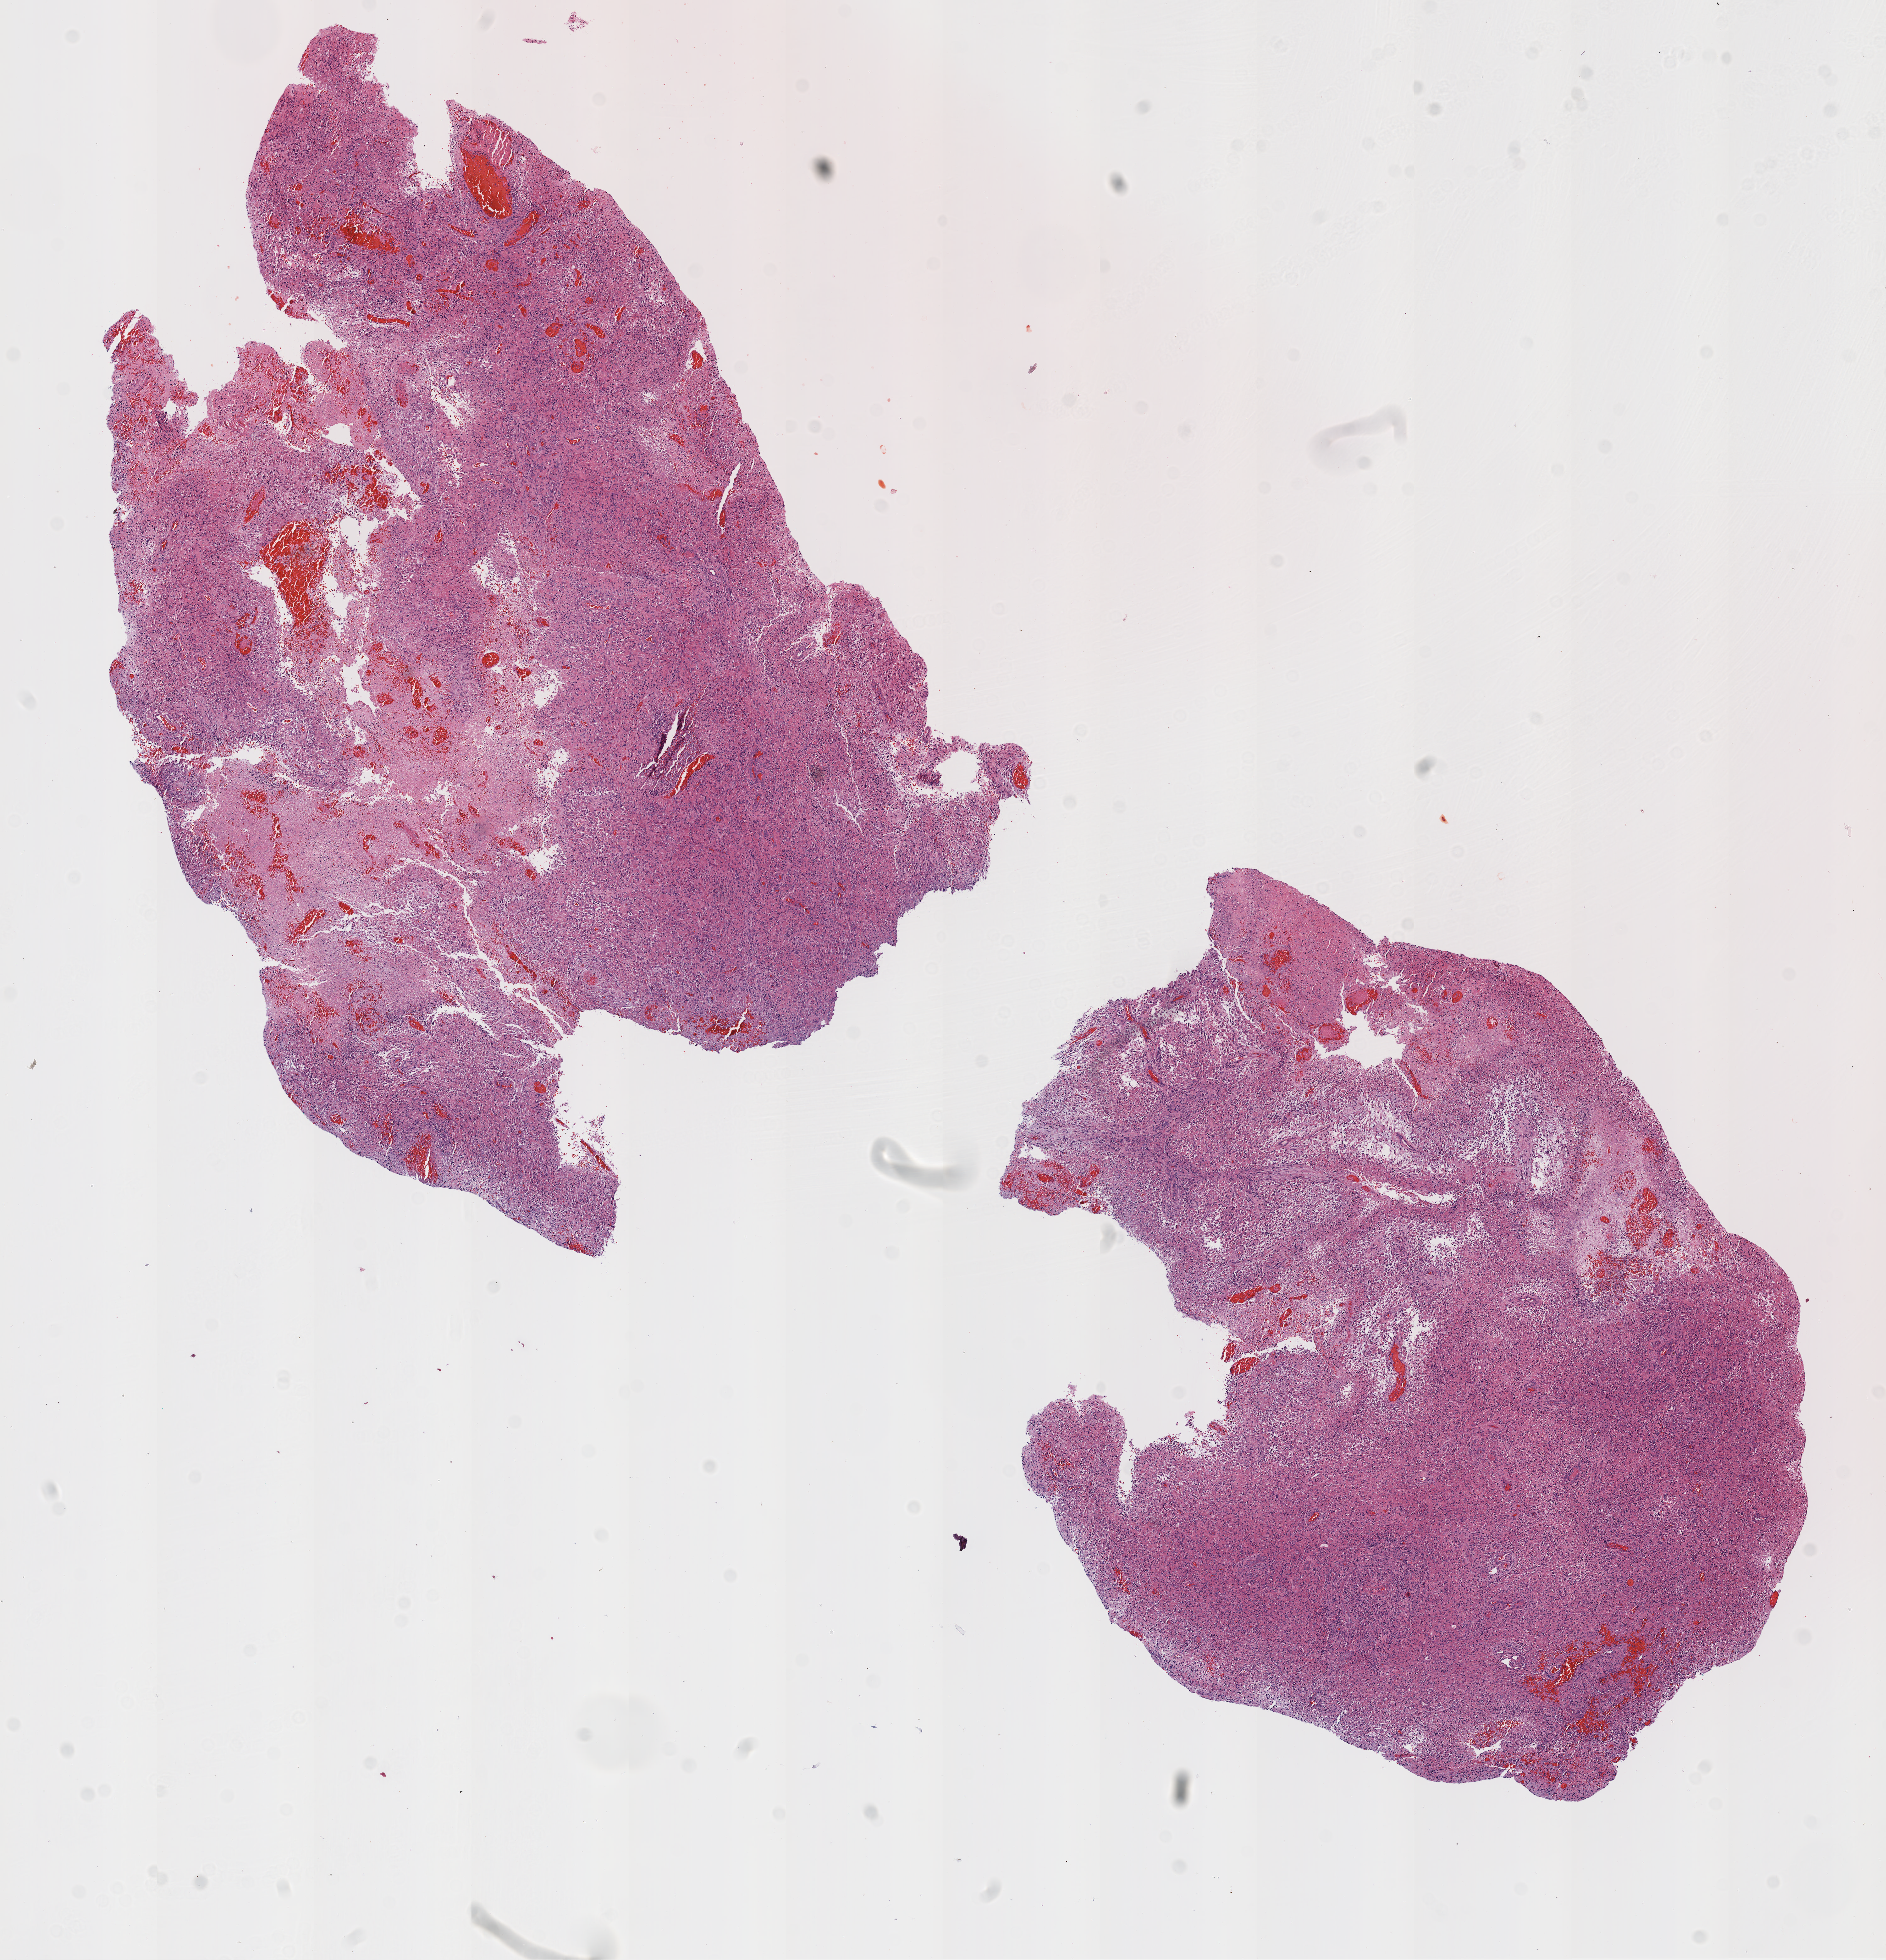
Digitized H&E tissue section (whole slide), whole scanned area (about 12.0 x 12.5 mm, slide scanned at 20x) shown as a low-resolution overview. Formalin-fixed paraffin-embedded (FFPE) diagnostic section. Brain, primary tumour sample. Male, age 64 years at initial diagnosis.
Histologic diagnosis: Glioblastoma.